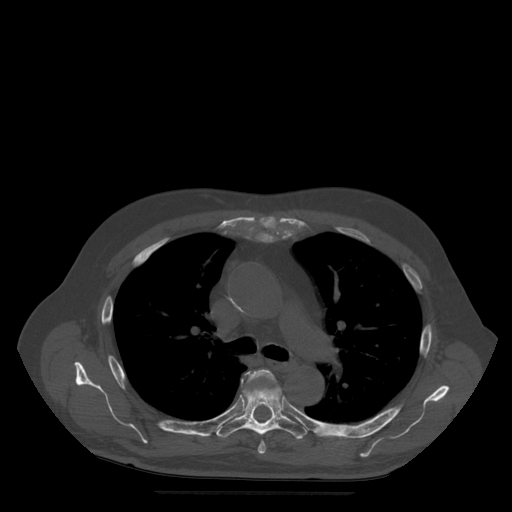
CT including the spine, one axial slice; position 359 of 522 along the scan axis; bone window (W 1800 / L 400 HU); 1.25 mm slice thickness; 512 × 512 image matrix, field of view 420 × 420 mm. Patient age 72 years. Case-level facts recorded for this patient, not image findings: primary cancer: prostate.
Outlined on this slice (semi-automatically segmented with operator editing):
- T5 vertebra: bounding box <248,370,275,454> (left, top, right, bottom; pixels)
- T6 vertebra: <217,370,308,440>